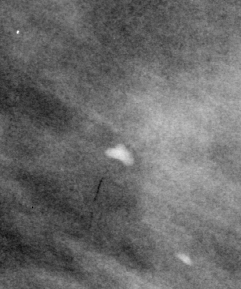
Cropped region of a digitized screen-film mammogram centred on a radiologist-marked abnormality, left breast, MLO view.
- Marked abnormality: calcifications, morphology vascular / coarse; BI-RADS assessment category 2; subtlety rating 3 on a 1 (subtle) to 5 (obvious) scale; benign without callback (not worked up further).